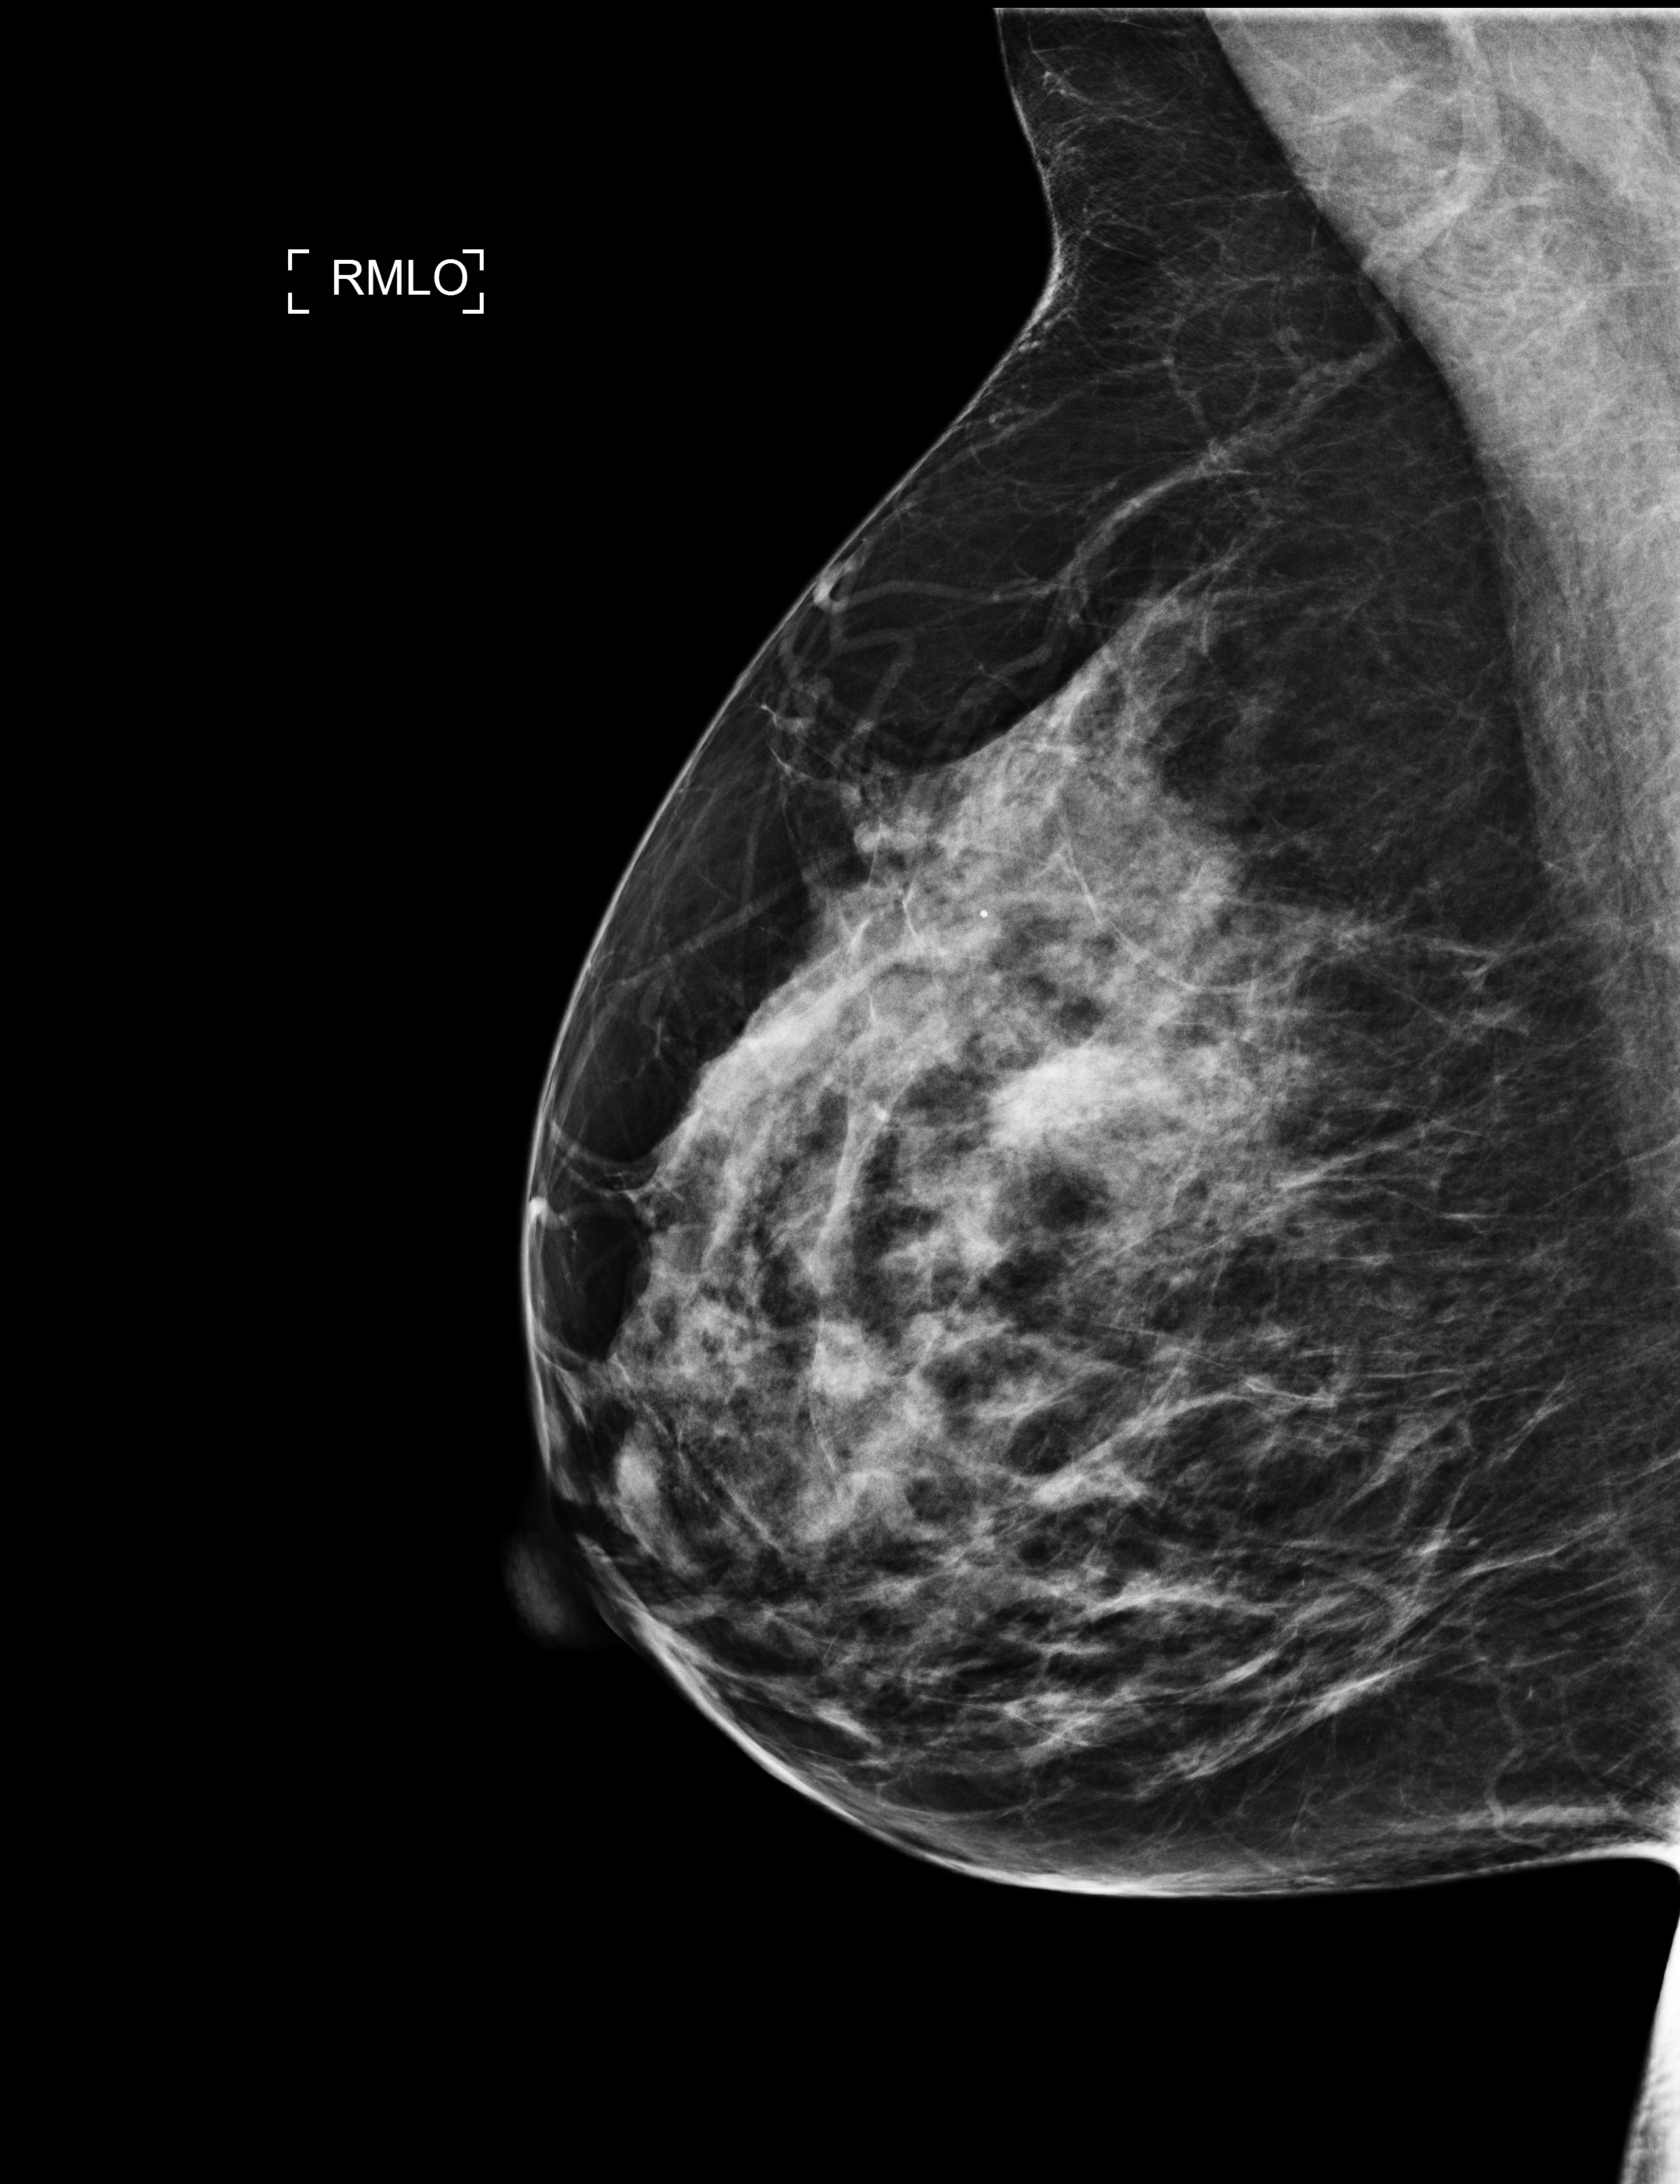
Full-field digital mammogram (FFDM), right breast, medio-lateral oblique projection, screening examination, compressed breast thickness 61 mm. Patient aged 41 years (female).
- breast density at the screening exam (both breasts): heterogeneously dense (BI-RADS density category c)
- final BI-RADS assessment for this screening round (tomosynthesis exam, both breasts): category 1
- recall: recalled for additional imaging after this screen